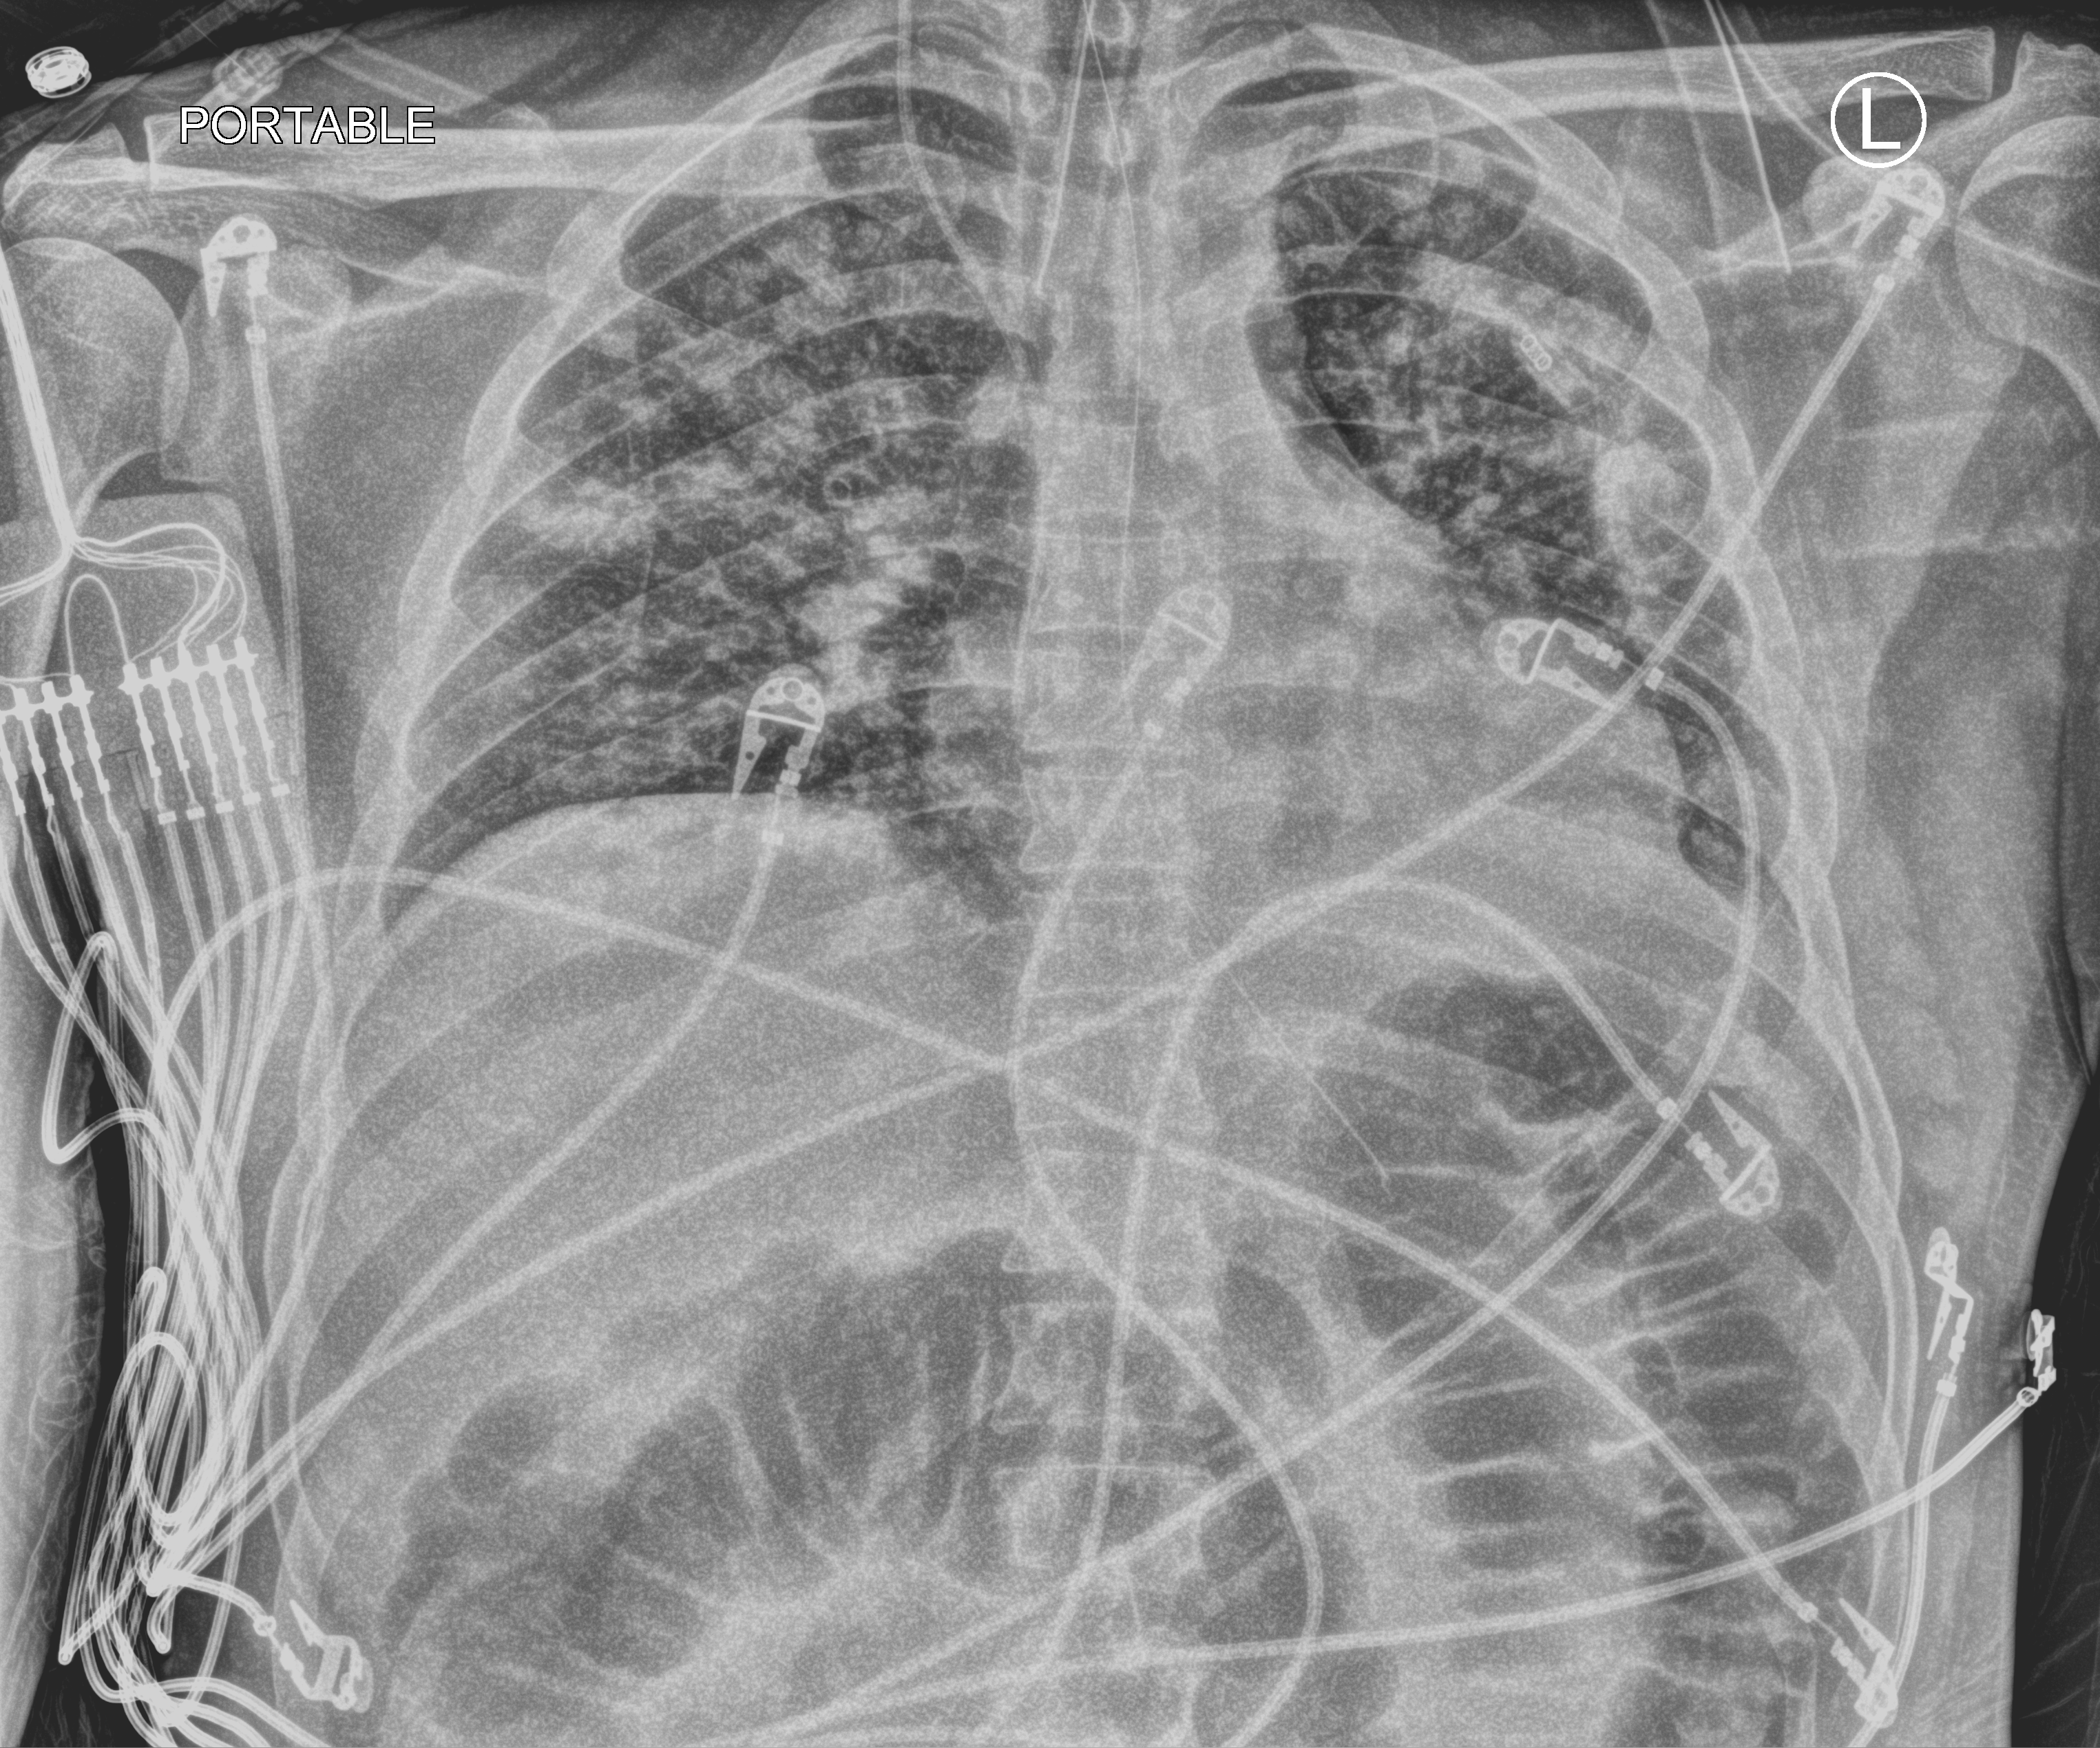
Portable chest radiograph, anteroposterior (AP) projection. Male patient hospitalised with COVID-19, age 18–59 years.
Admission-level facts for this patient (not findings on this image; timing relative to this image not recorded):
- diabetes (admission record): no